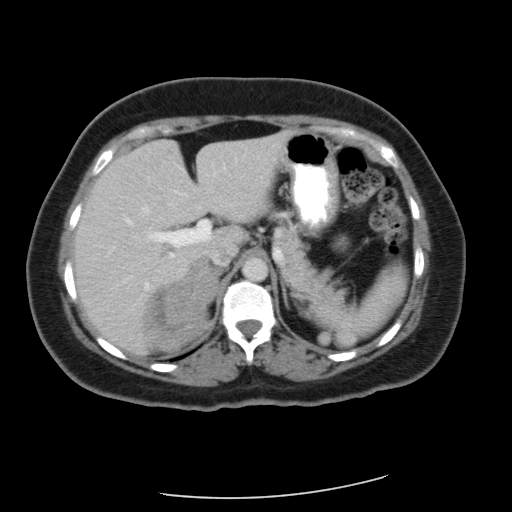
Contrast-enhanced abdominal CT, one axial slice; slice 40 of 56 in the series (ordered by position); reconstruction kernel FC12; soft-tissue window (W 400 / L 40 HU); 5 mm slice thickness; 512 × 512 image matrix, field of view 400 × 400 mm. Female patient, age 58 years. Case-level facts recorded for this patient, not image findings: diagnosis: adrenocortical carcinoma; tumour side: right adrenal; tumour size at pathology: 9 cm; Ki-67 index: 25 %; stage (as recorded): 3.
Structures marked on this image (semi-automatically segmented with operator editing):
- mass: box from (x=147, y=261) to (x=217, y=350) px